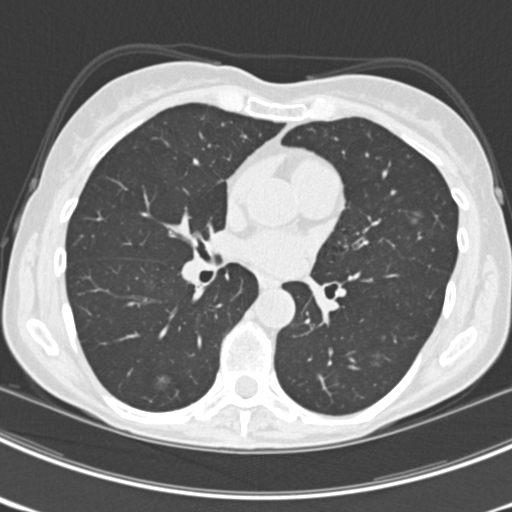
Axial slice from a low-dose chest CT screening exam; third screening round (two years after baseline); lung window (W 1500 / L -600 HU); 2 mm slice thickness; 120 kVp; slice 102 of 225 in the series. Female participant, aged 63 years at enrolment. Current smoker at enrolment.
- Expert-annotated lung lesion, box from (x=402, y=200) to (x=438, y=238) px.
- The screening reader recorded 9 non-calcified nodules or masses ≥4 mm on this exam (left upper lobe, right upper lobe, left upper lobe, left lower lobe, right middle lobe, left lower lobe, left lower lobe, right lower lobe, right lower lobe); which of them this box marks is not recorded.
- Lung cancer was diagnosed 15 days after this screen: bronchiolo-alveolar adenocarcinoma, NOS, right upper lobe, right middle lobe, right lower lobe, left upper lobe, left lower lobe, moderately differentiated (G2), stage IV (AJCC 6th edition).